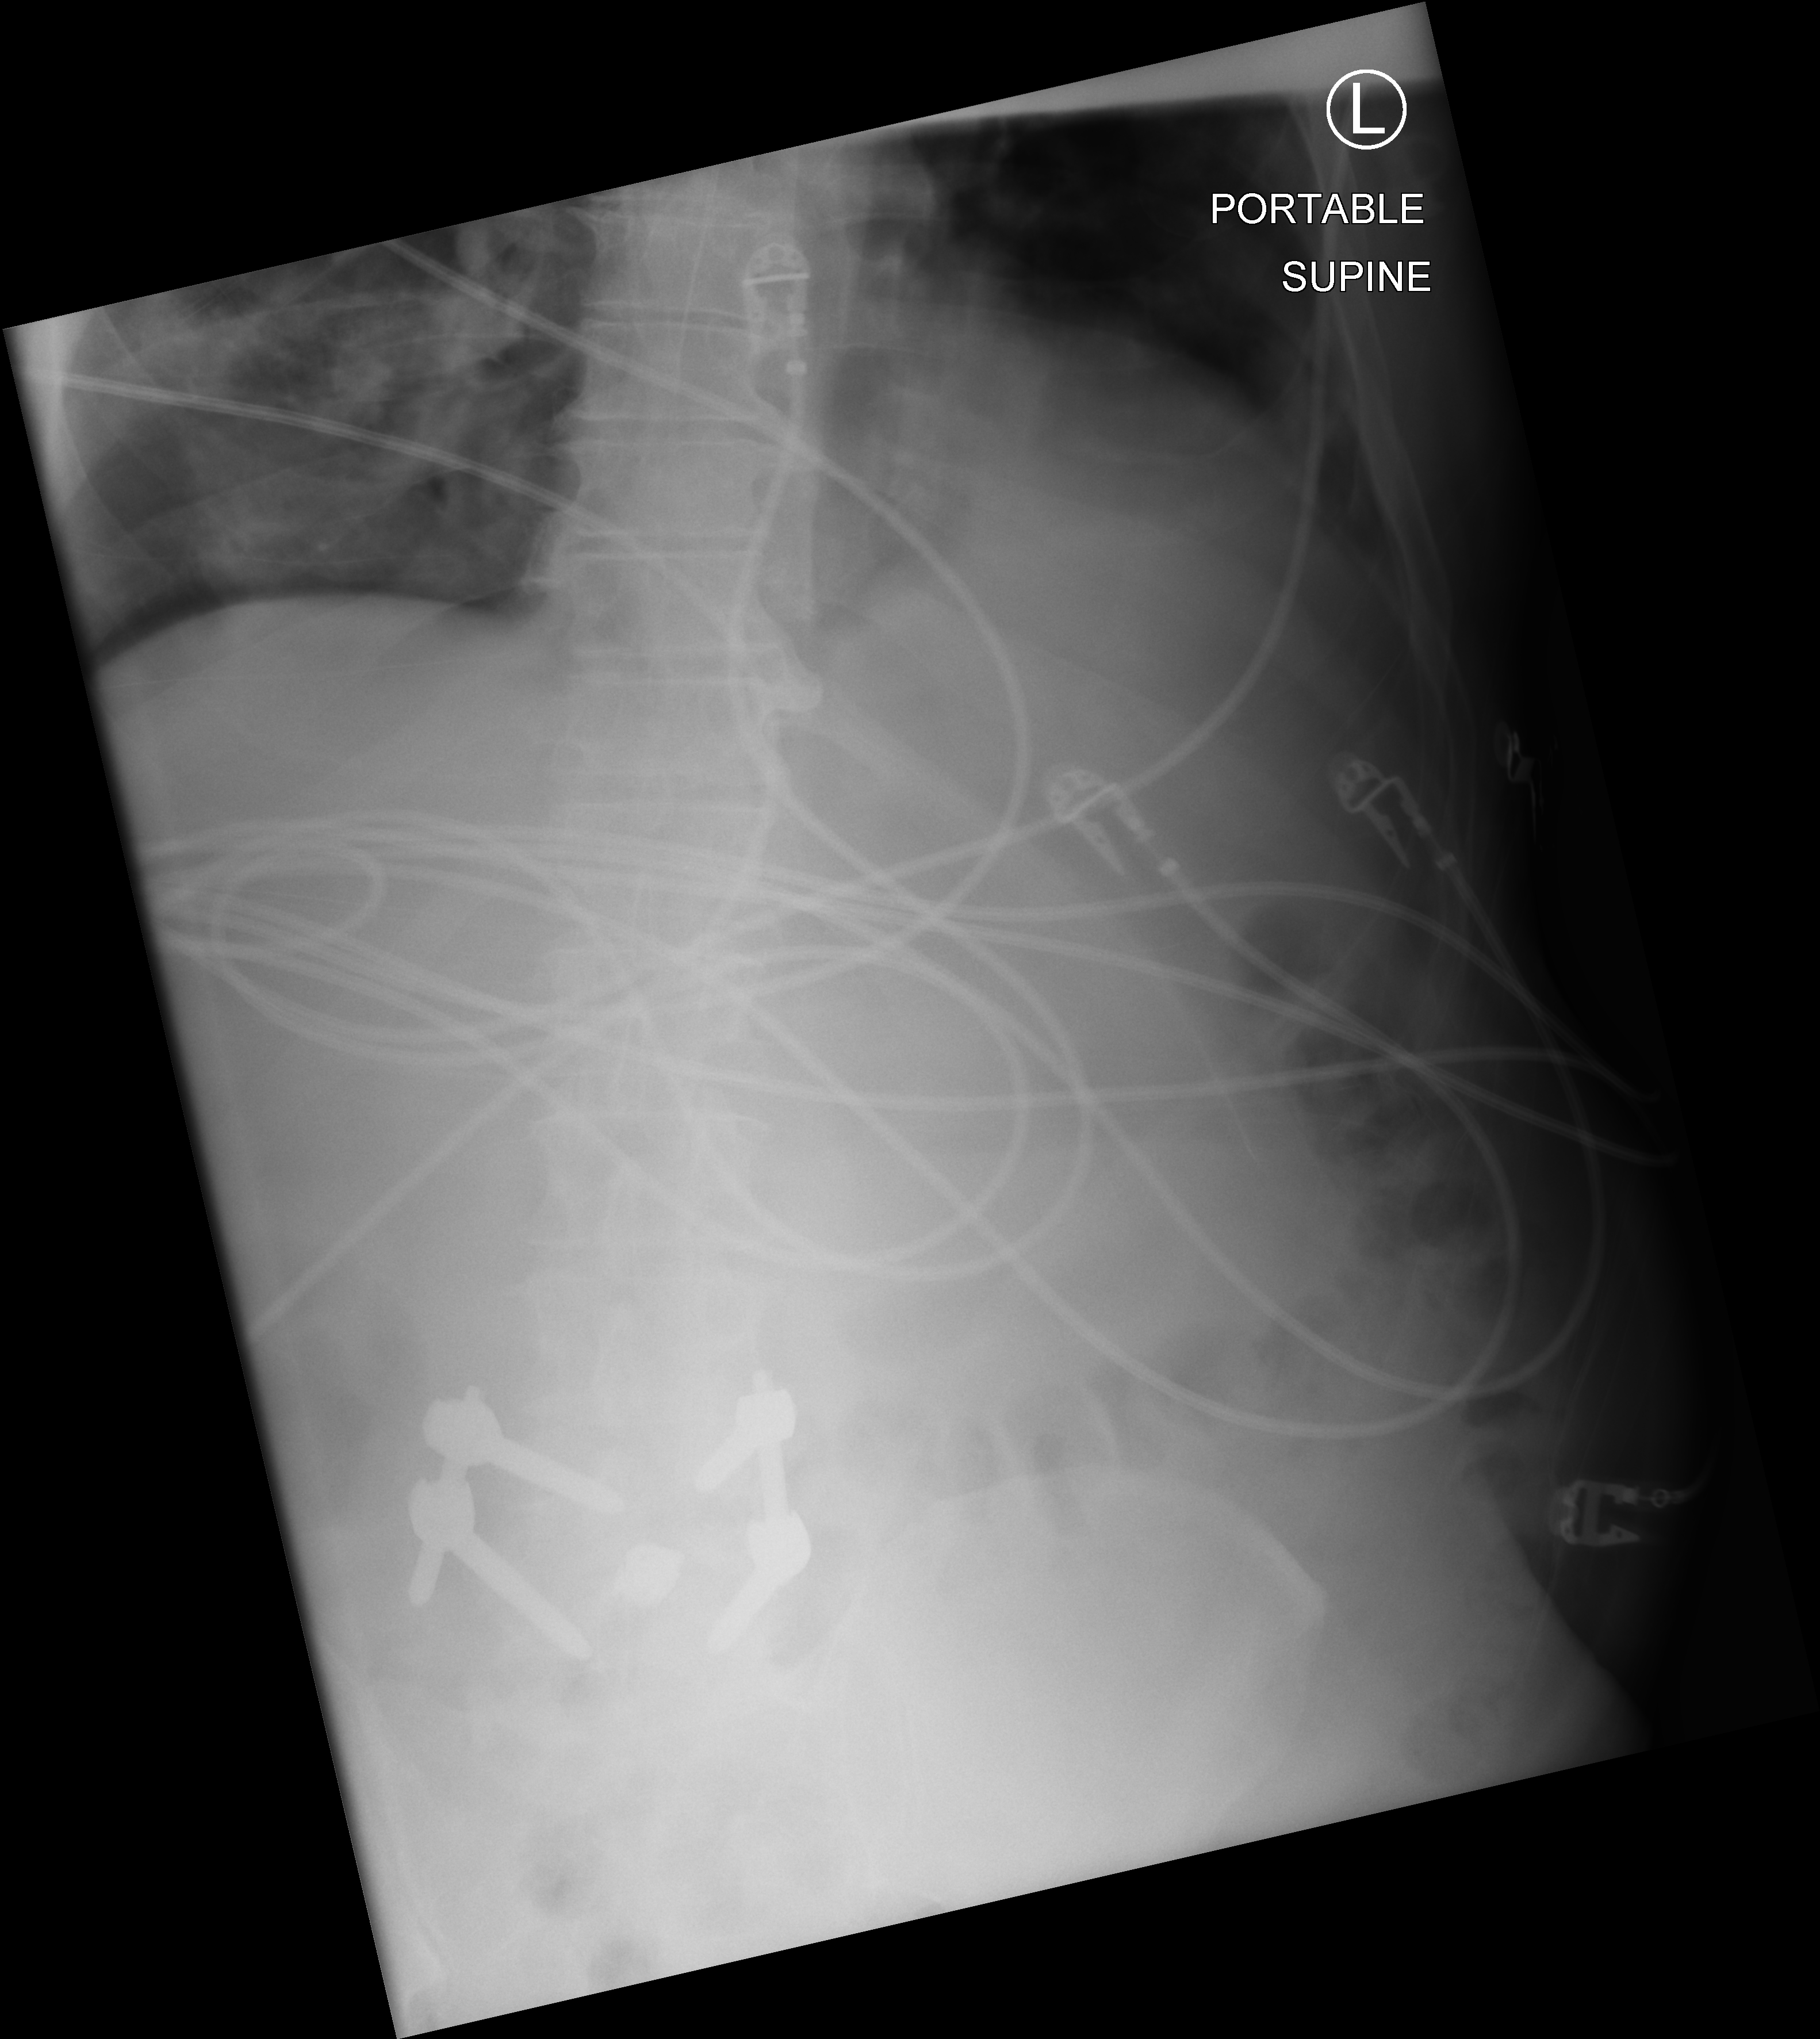
Portable abdomen radiograph. Male patient hospitalised with COVID-19, age 60–74 years.
Admission-level facts for this patient (not findings on this image; timing relative to this image not recorded): diabetes (admission record): yes; mechanically ventilated during this hospital stay: yes.